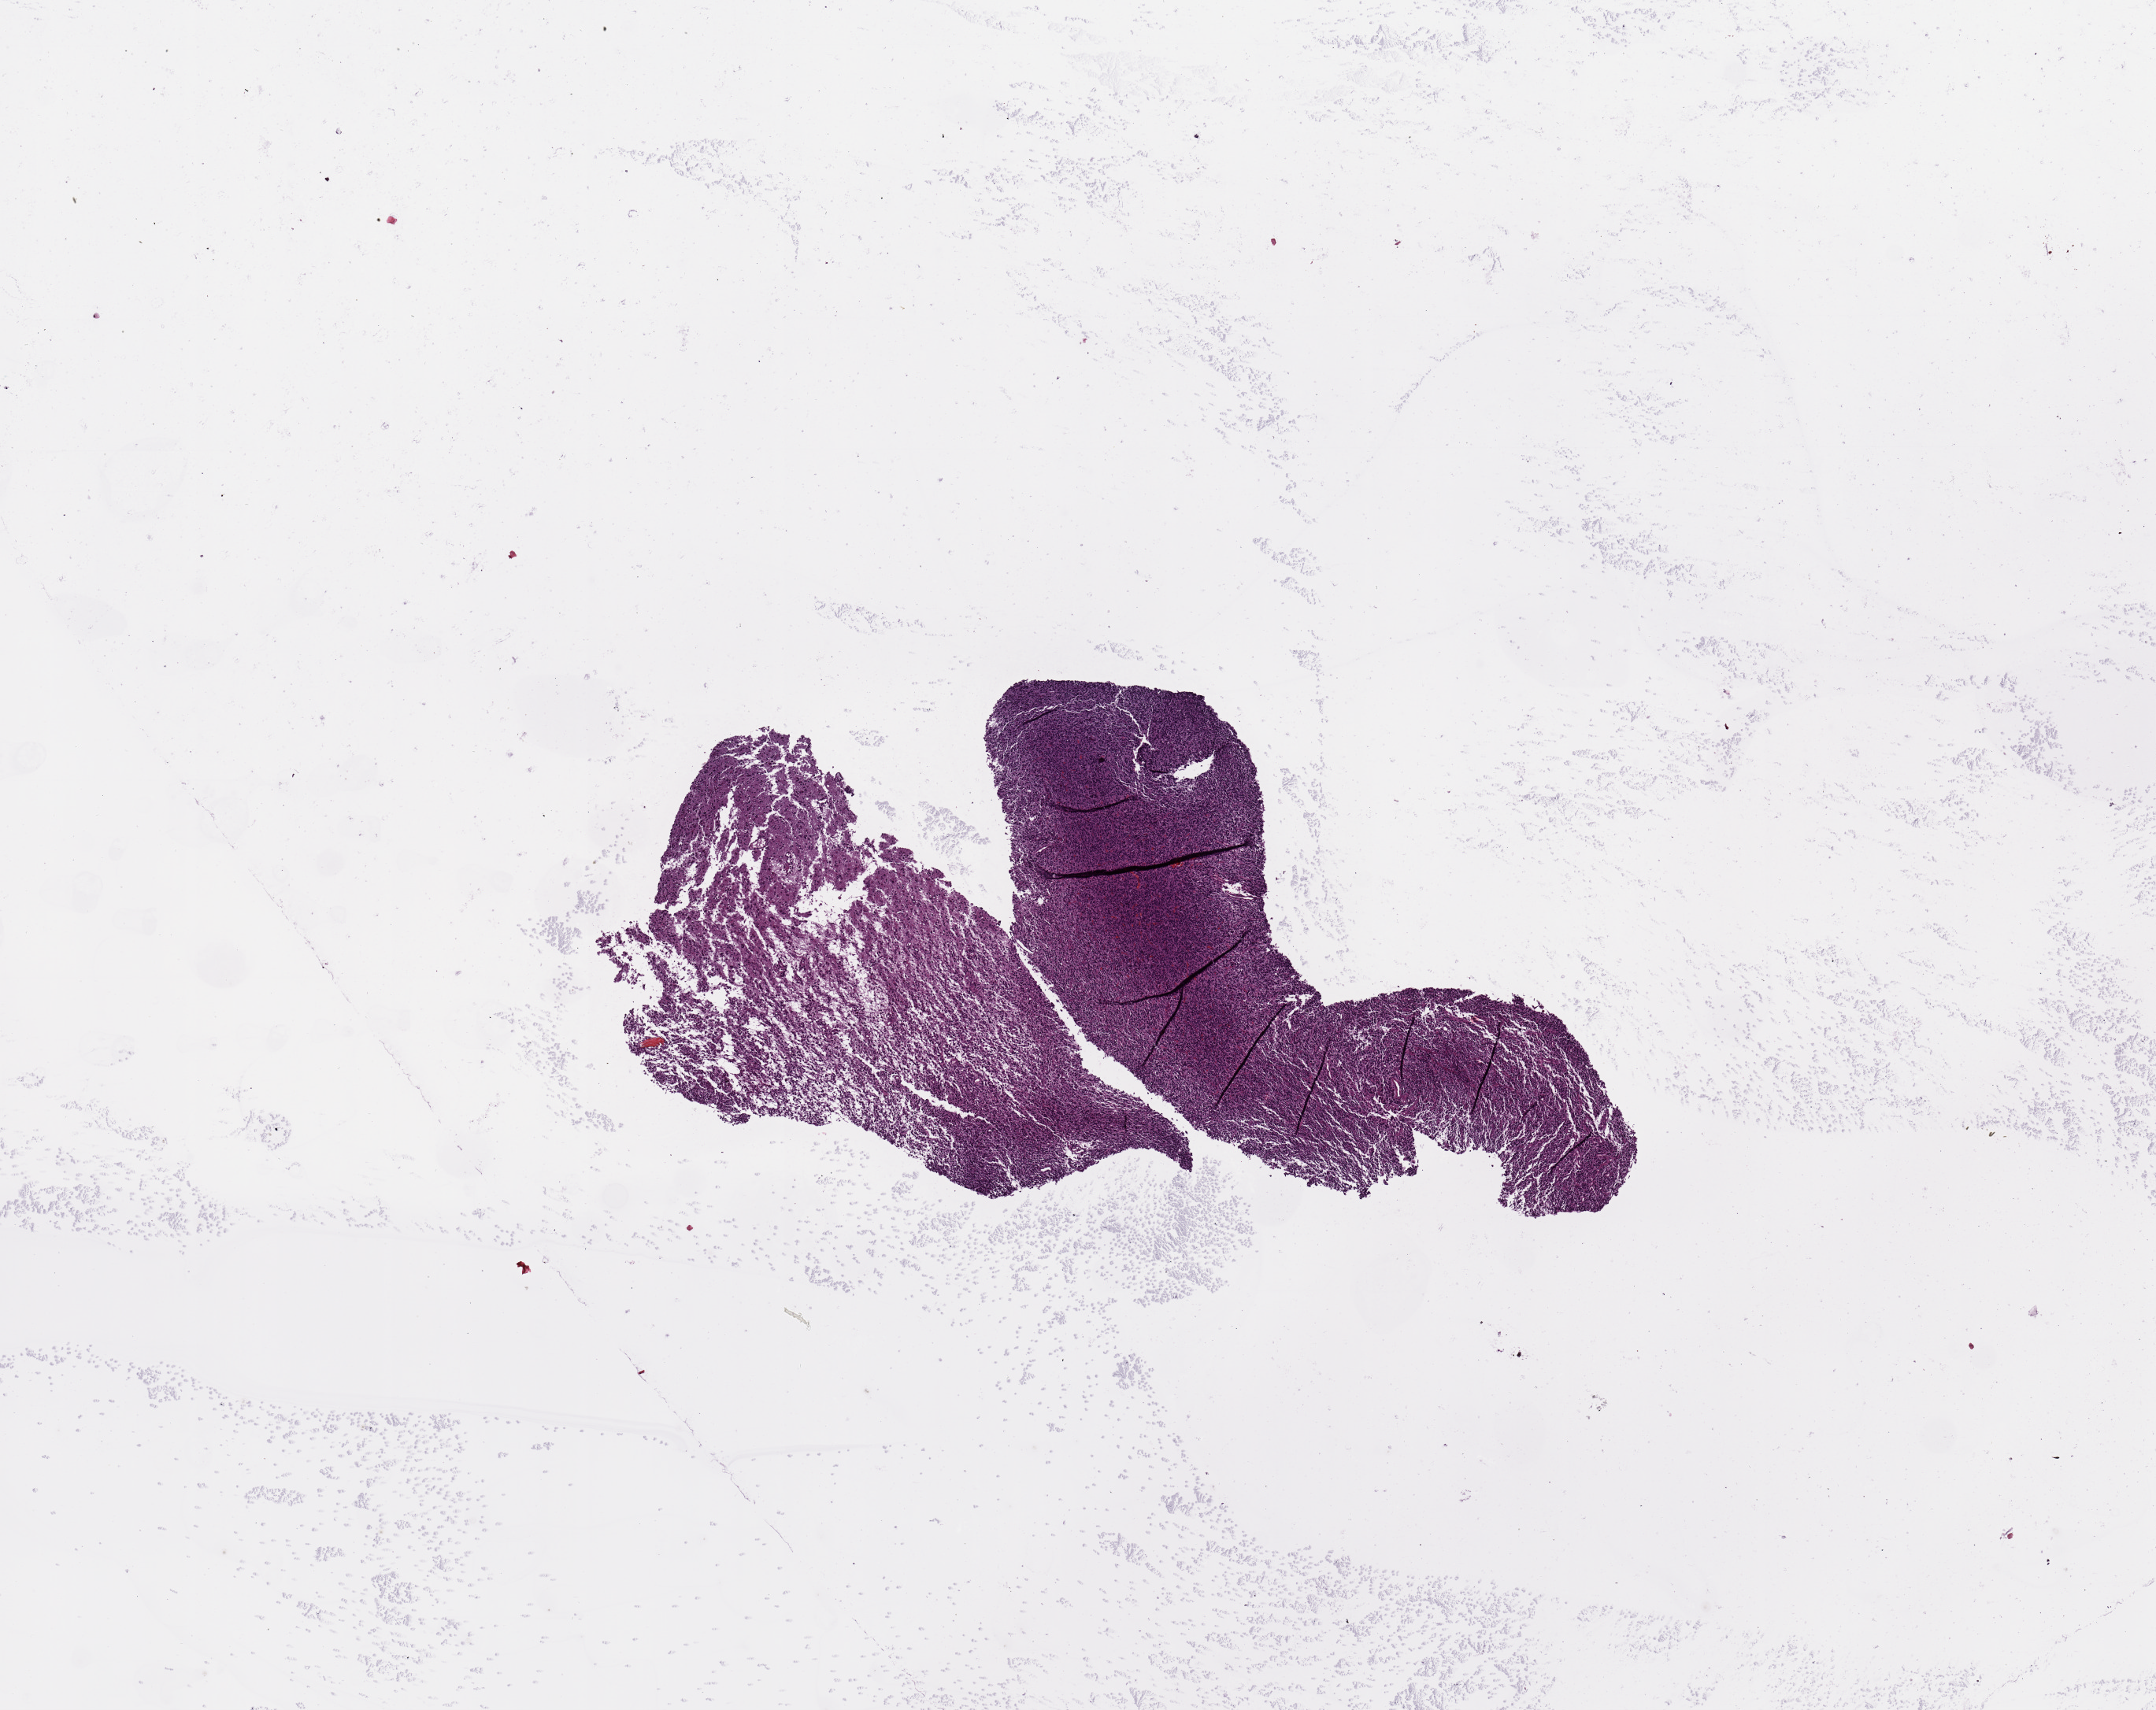
Whole-slide histology image, H&E, shown as a low-resolution overview of the whole scanned area (about 10.8 x 8.6 mm), brain, tumour tissue. Patient: male, age 35 years.
Diagnosis: Glioblastoma.